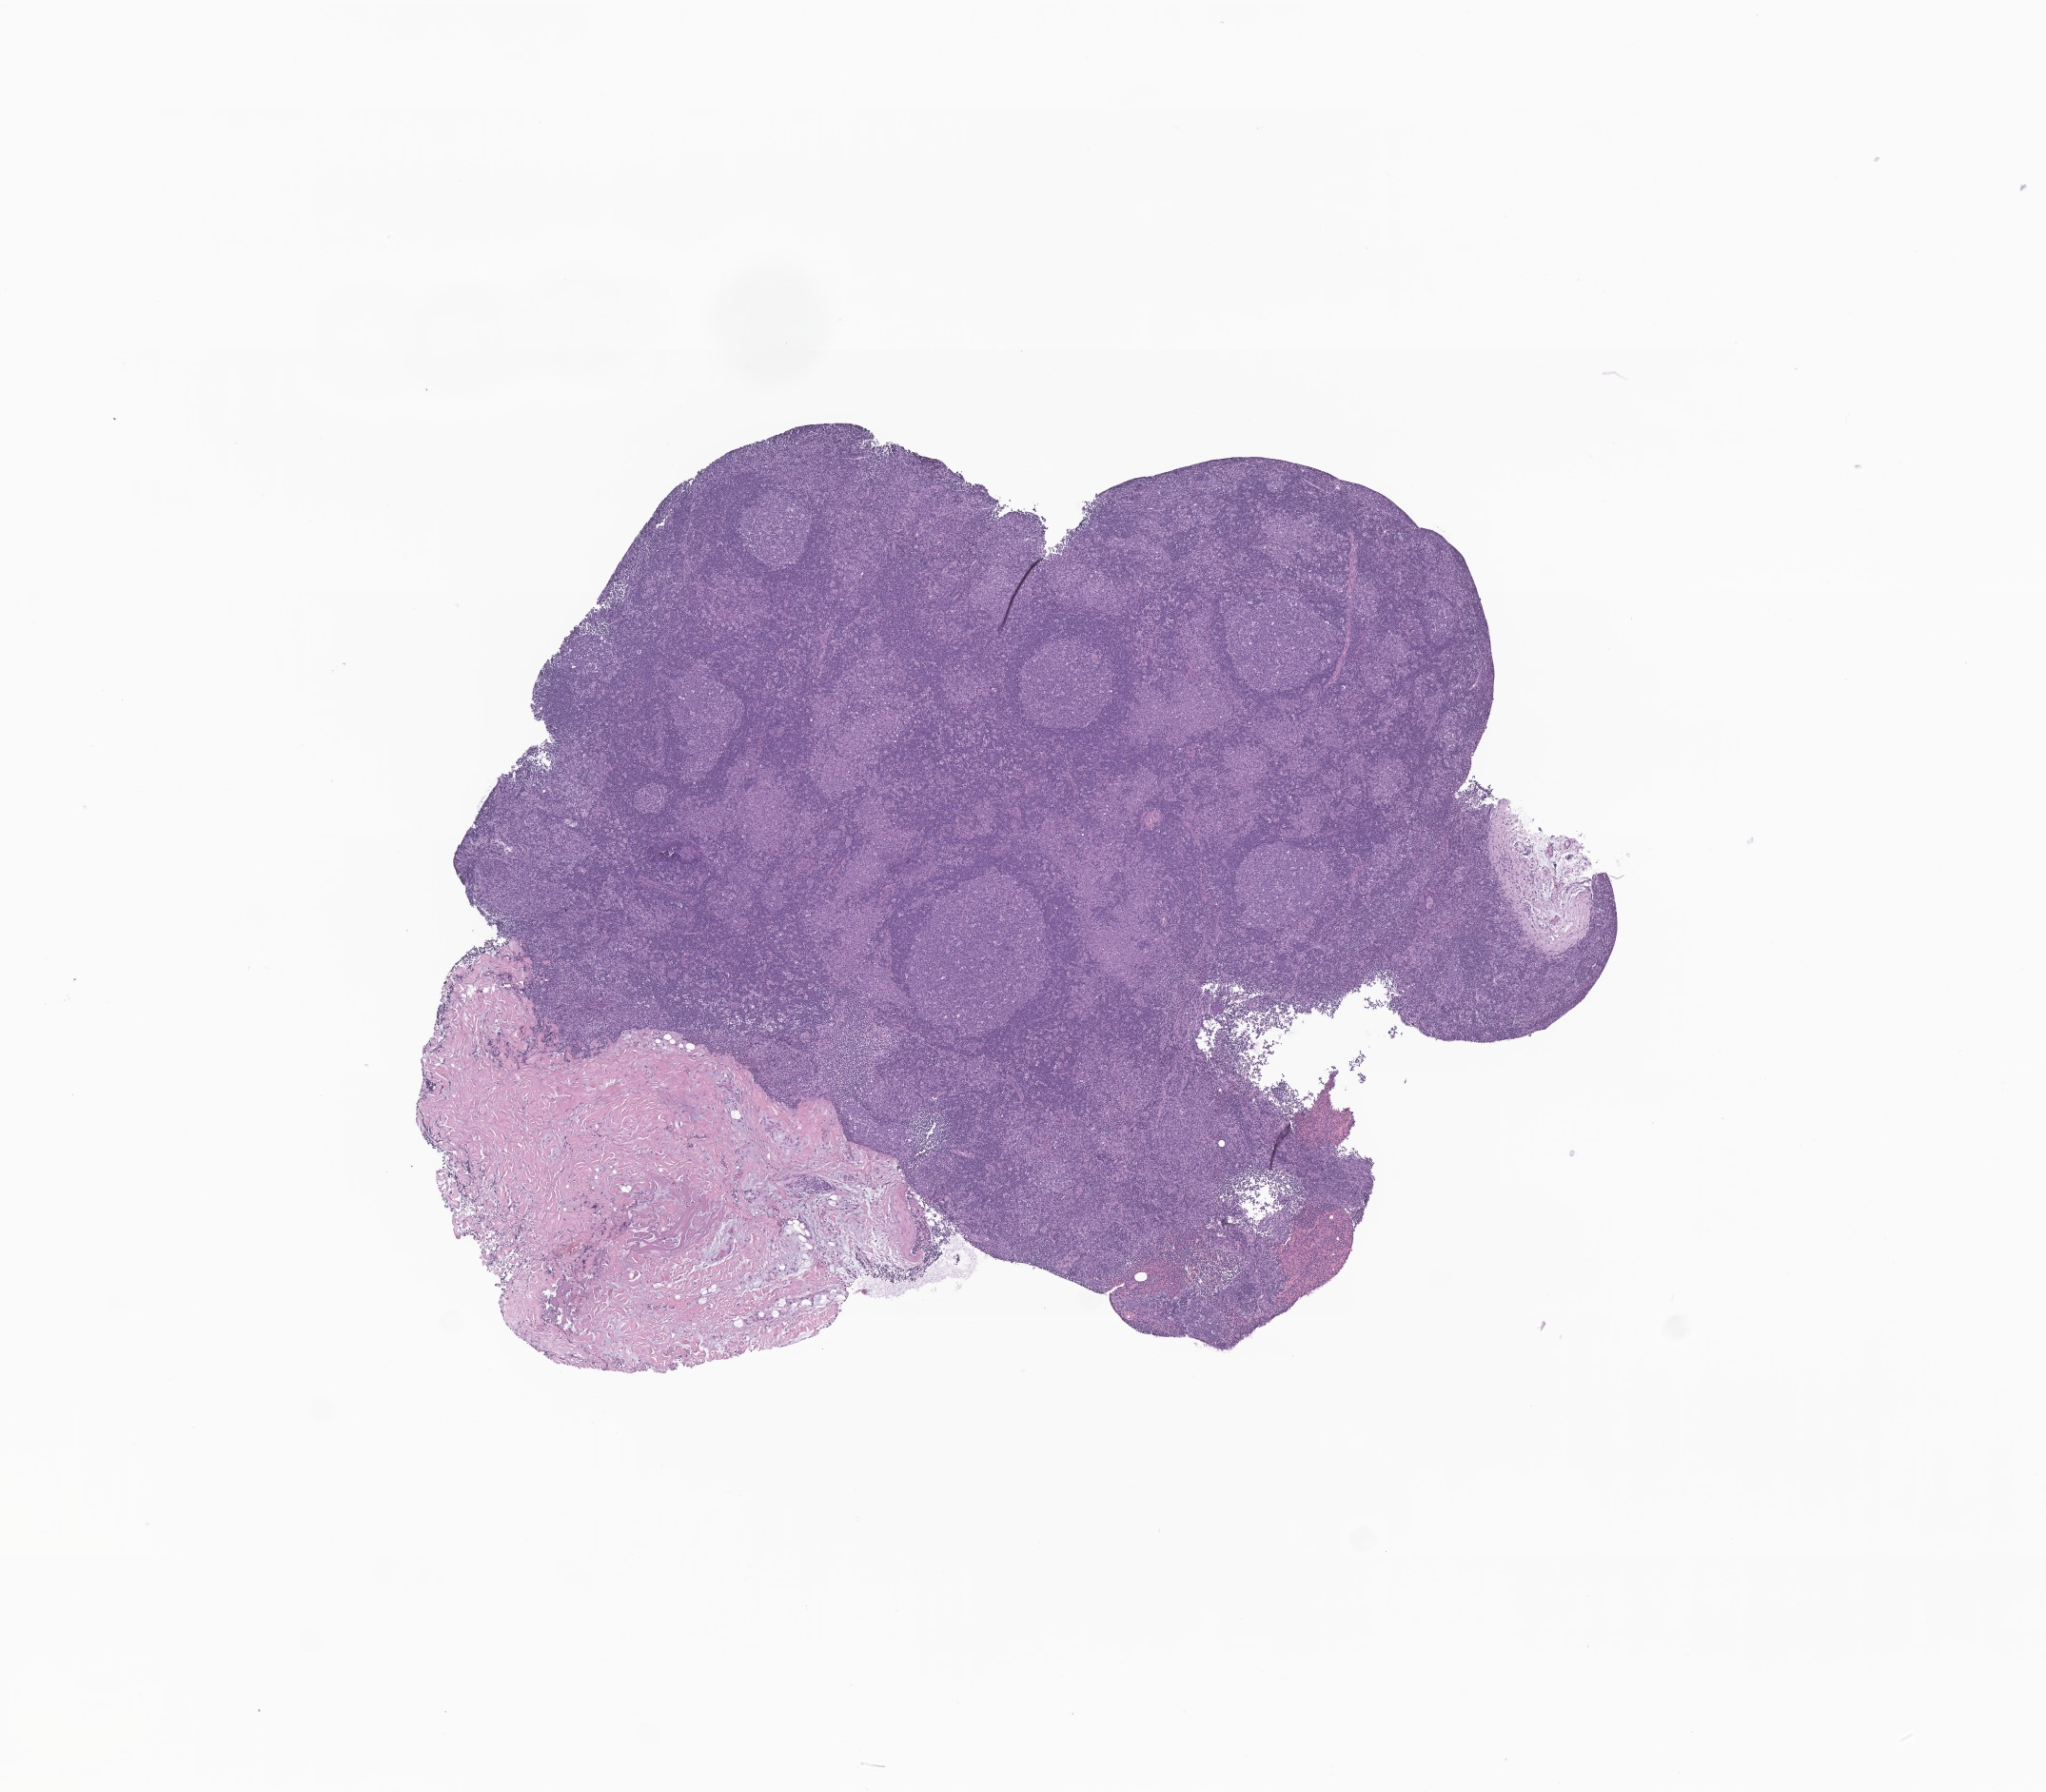
Haematoxylin and eosin whole-slide image of tumor tissue from the head and neck lymph node, whole scanned area (about 9.1 x 7.9 mm) shown as a low-resolution overview, FFPE section. Male patient, age 181 months (15 years 1 month).
- recorded diagnosis: Squamous cell carcinoma, NOS
- tissue or organ of origin (case record): lymph nodes of head, face and neck